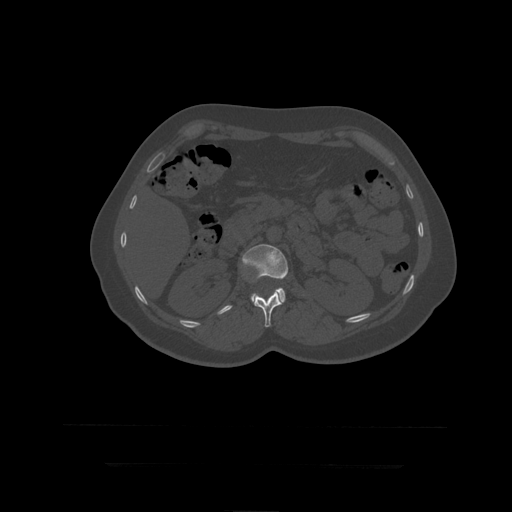
CT including the spine, one axial slice; slice 163 of 399 in the series (ordered by position); reconstruction kernel STANDARD; bone window (W 1800 / L 400 HU); 1.25 mm slice thickness; 512 × 512 image matrix, field of view 450 × 450 mm. Patient age 41 years. Case-level facts recorded for this patient, not image findings: primary cancer: breast.
Structures marked on this image (semi-automatically segmented with operator editing):
- L1 vertebra: bounding box <251,291,283,328> (left, top, right, bottom; pixels)
- L2 vertebra: <242,244,289,303>